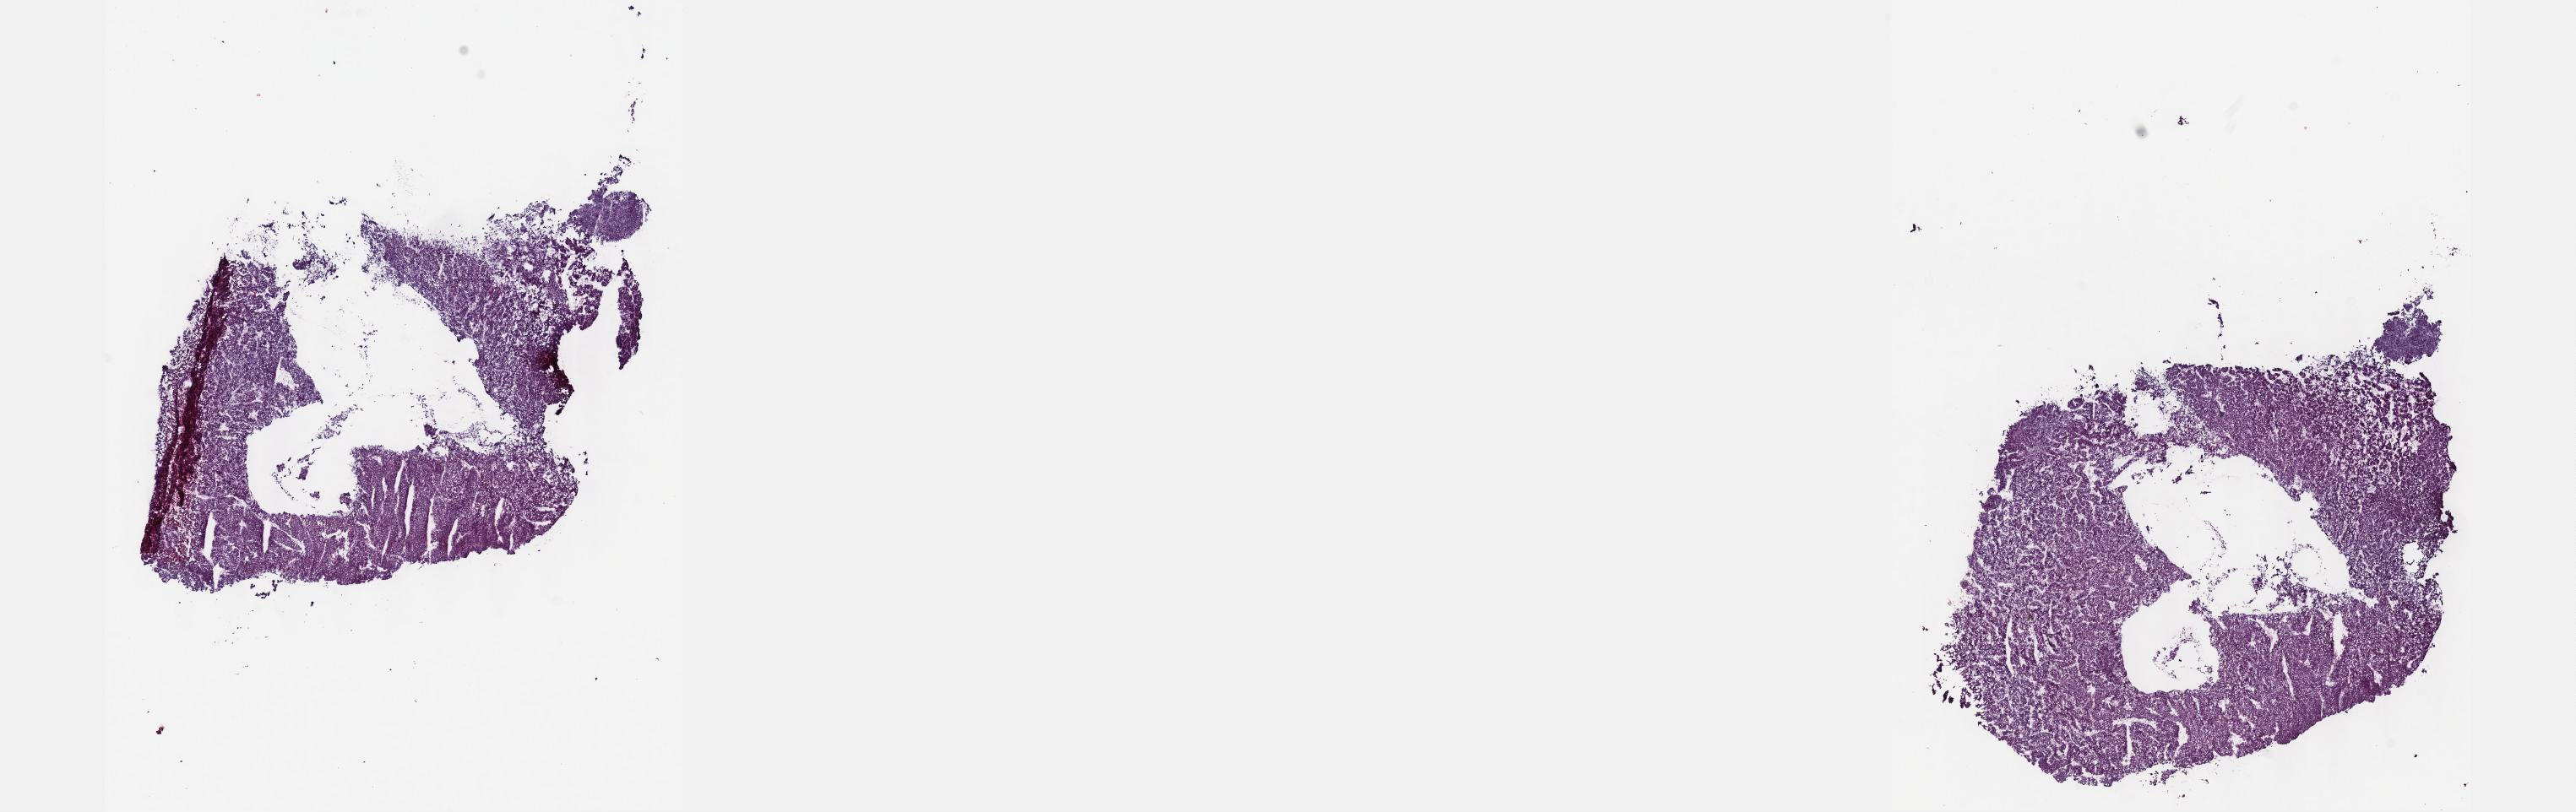
Whole-slide histology image, H&E-stained — whole scanned area (about 24.6 x 7.8 mm, slide scanned at 40x) shown as a low-resolution overview, frozen section, sample: recurrent tumour, liver. Patient: male, age at initial diagnosis 65 years. Slide review estimates, as recorded: tumour cells 80%, tumour nuclei 80%, normal cells 0%, stromal cells 20%, necrosis 0%. Infiltration values recorded for this section: lymphocyte infiltration 3%, monocyte infiltration 2%, neutrophil infiltration 5%.
• this section: recurrent tumour
• patient diagnosis: Hepatocellular carcinoma, NOS